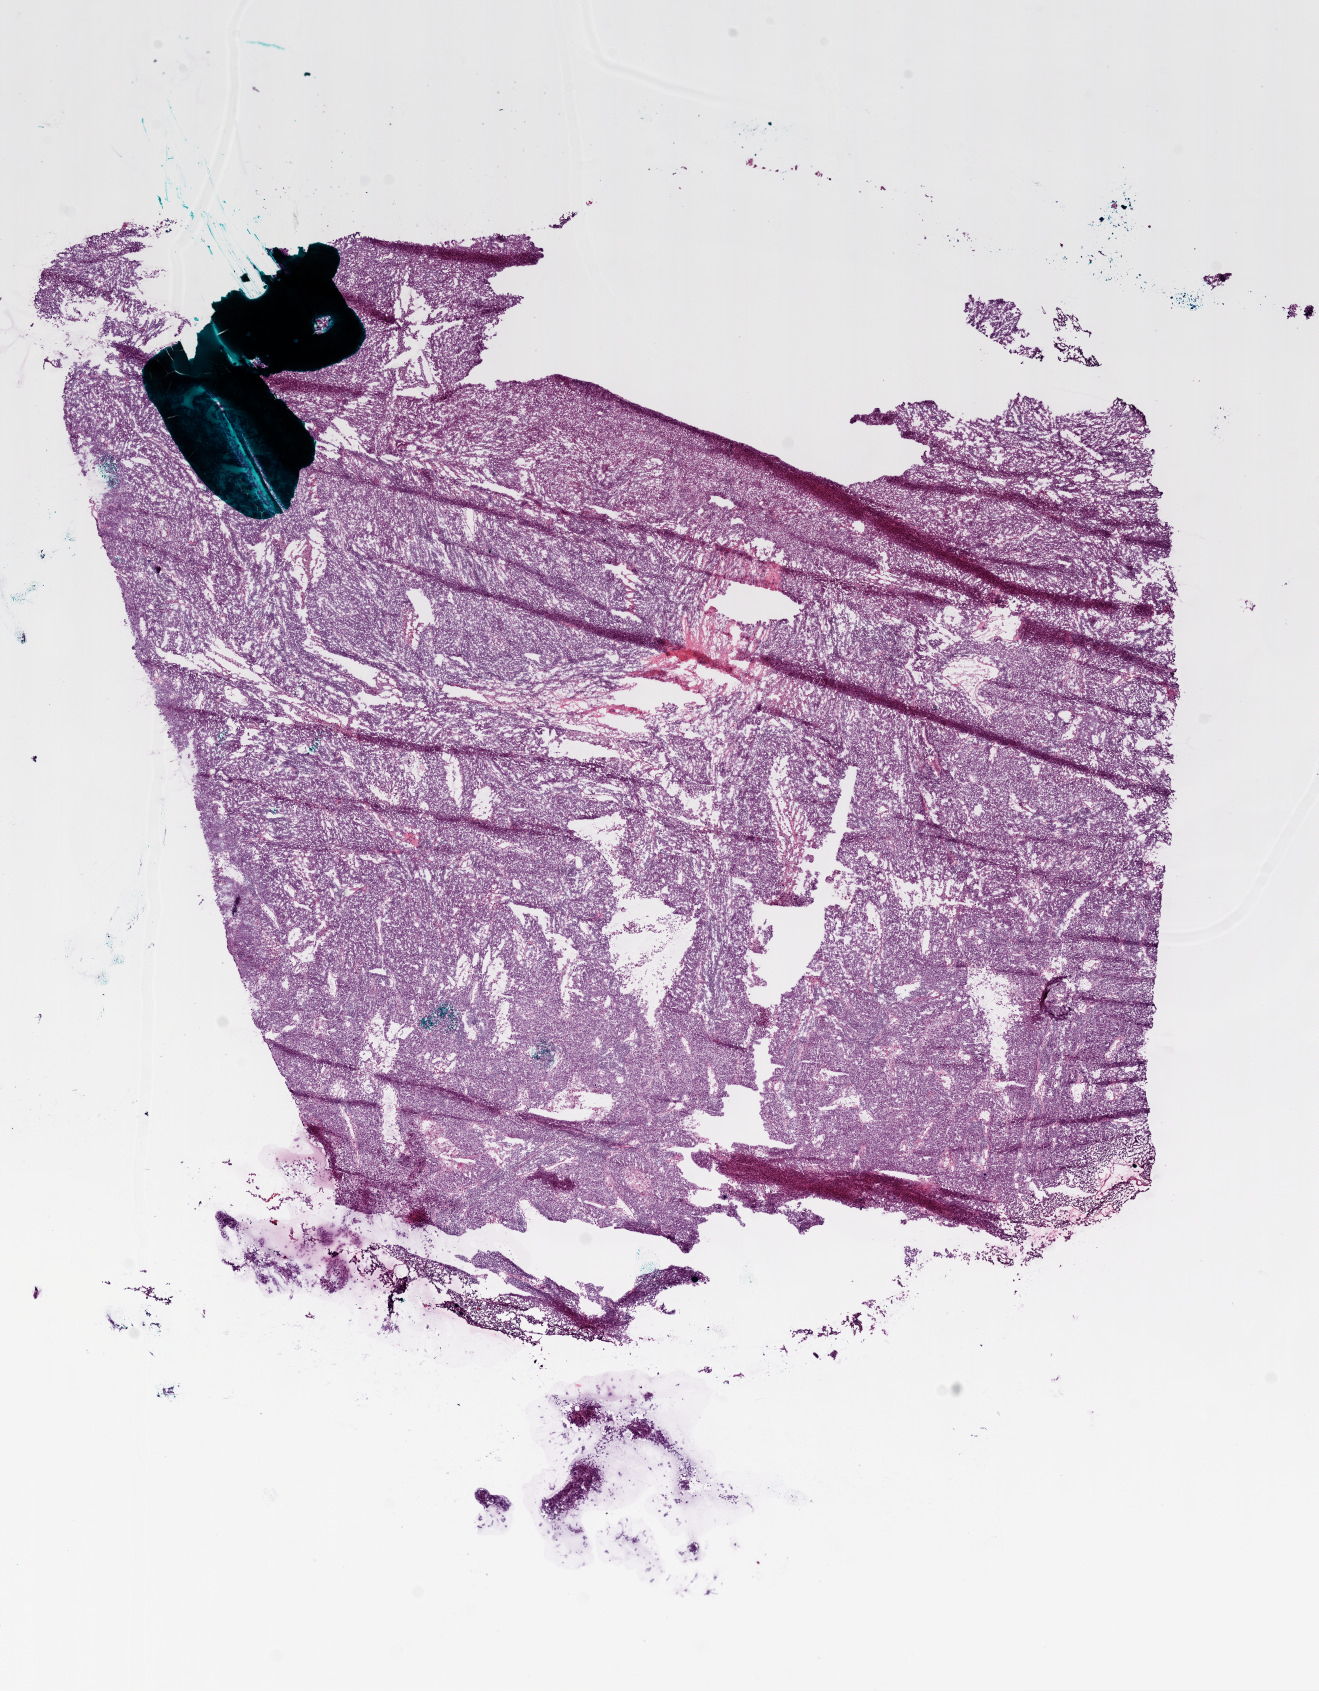
H&E whole-slide image — low-resolution overview of the scanned area, about 10.6 x 13.6 mm; frozen section from the bottom of the tissue portion; primary tumour sample from the ovary. Female, age 78 years at initial diagnosis.
Histologic diagnosis: Serous cystadenocarcinoma, NOS.